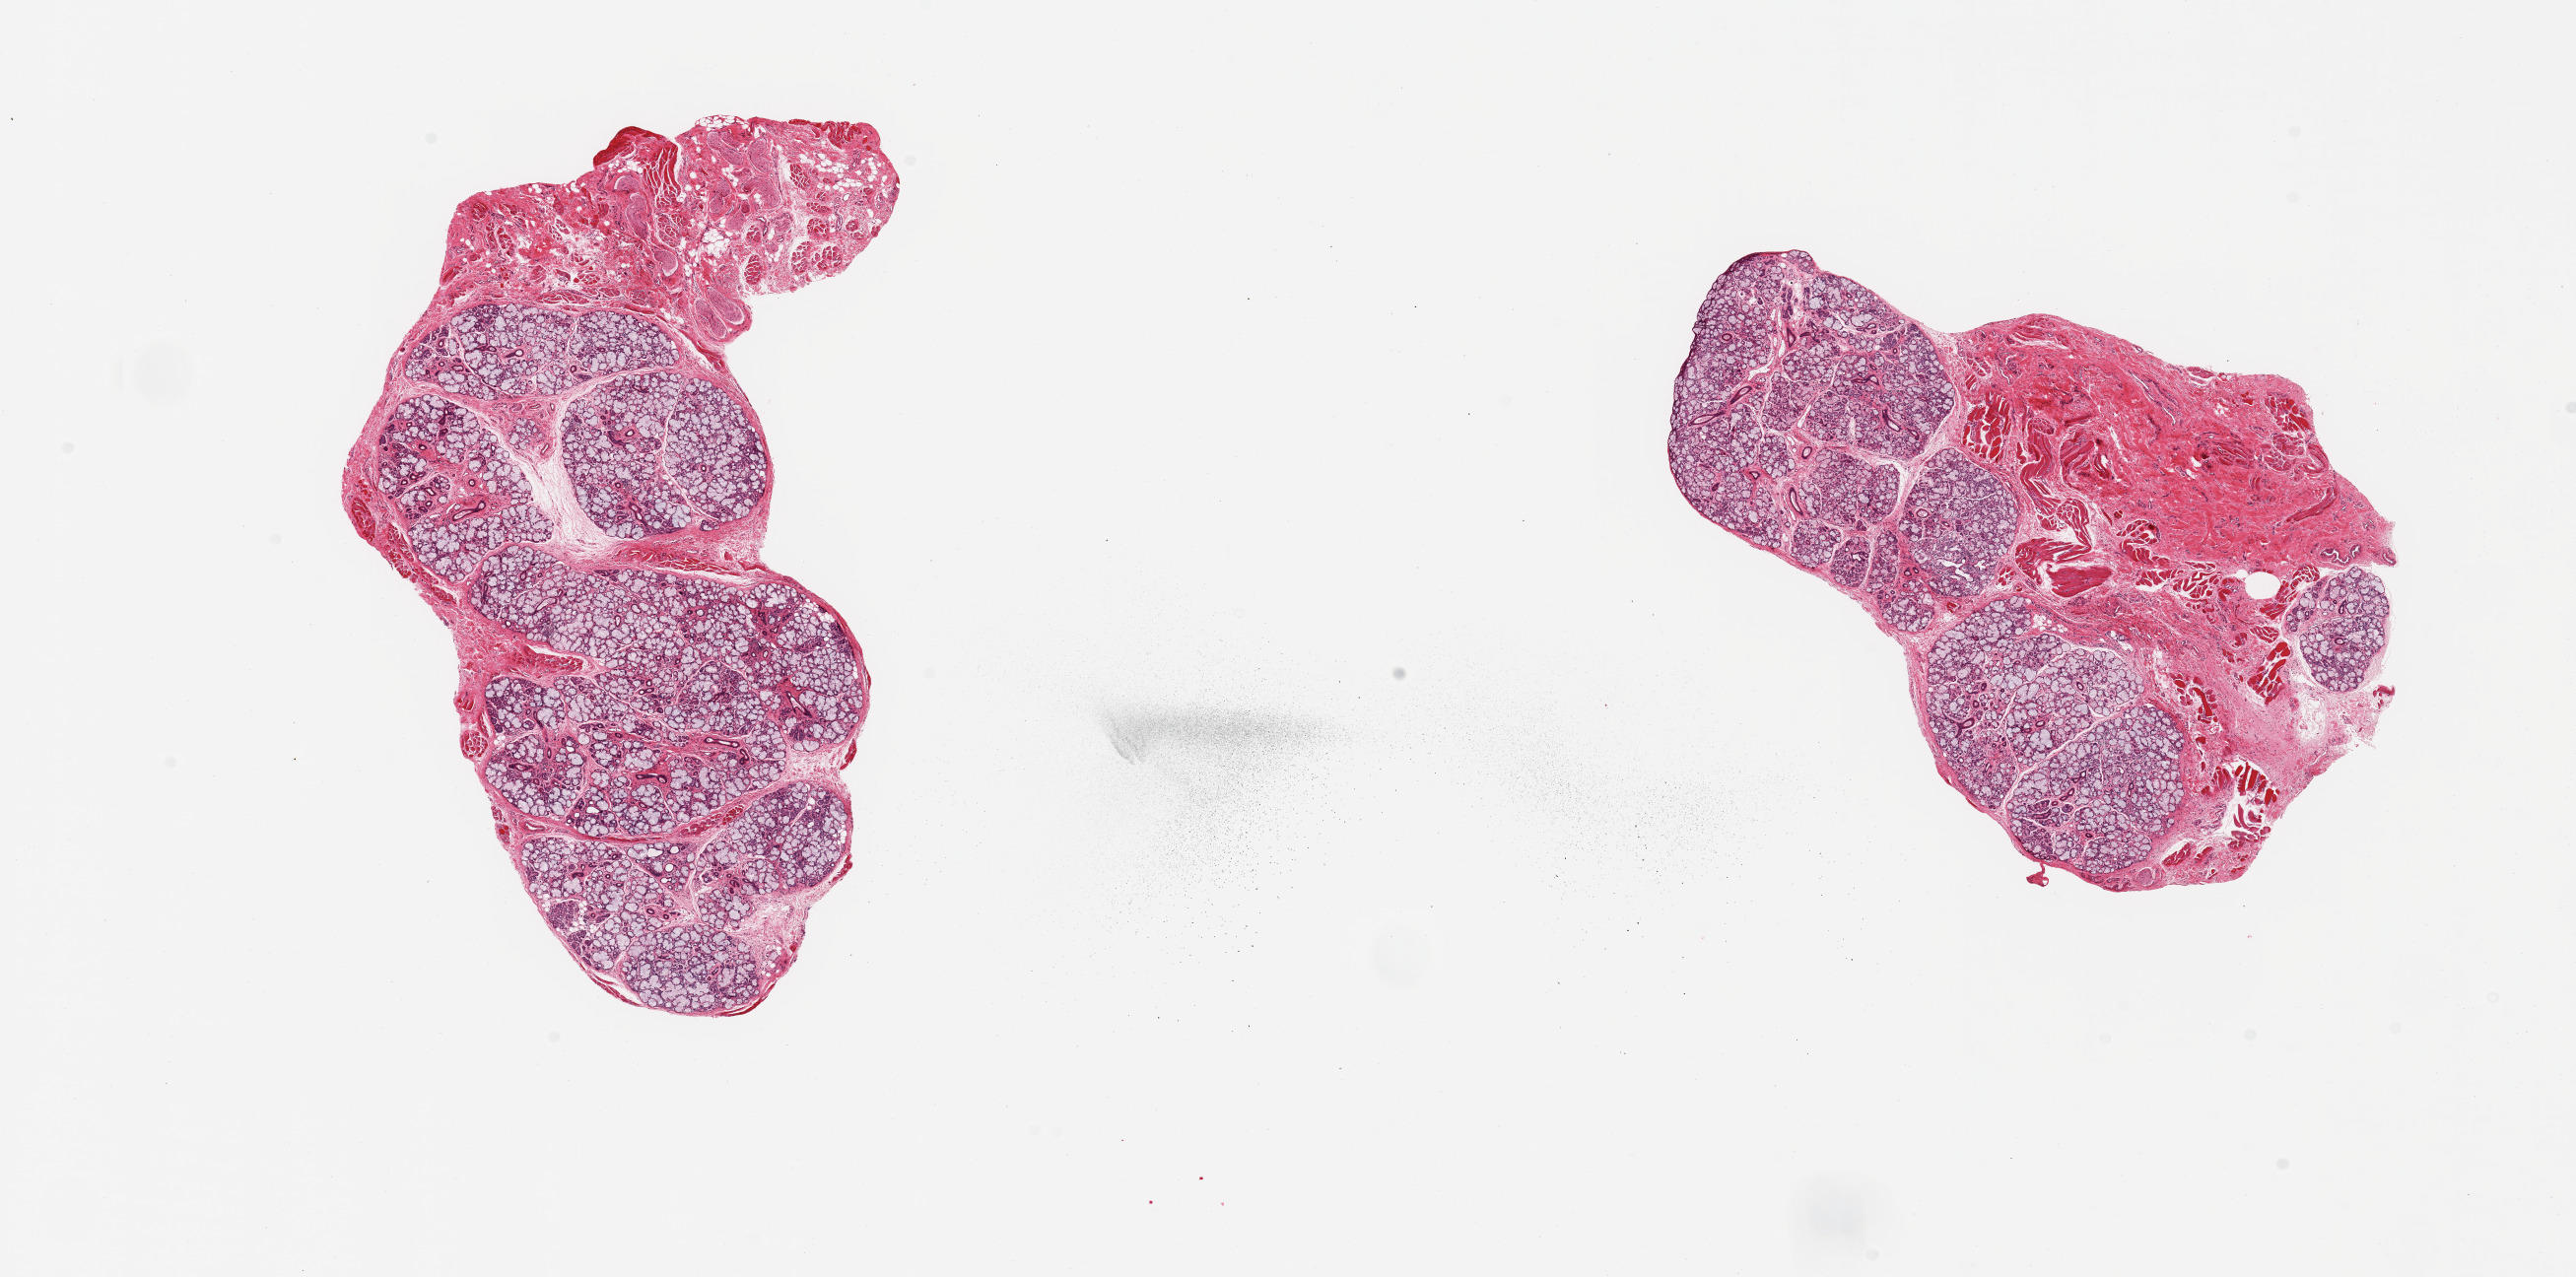
Whole-slide image, H&E stain, low-resolution overview of the scanned area, about 20.7 x 10.2 mm. PAXgene-fixed paraffin-embedded (PFPE) section. Sampled site (target tissue): minor salivary gland. Donor tissue sample. Male donor.
Review note (as recorded): 2 pieces, ~75% glandular parenchyma; rest is stroma/skeletal muscle.